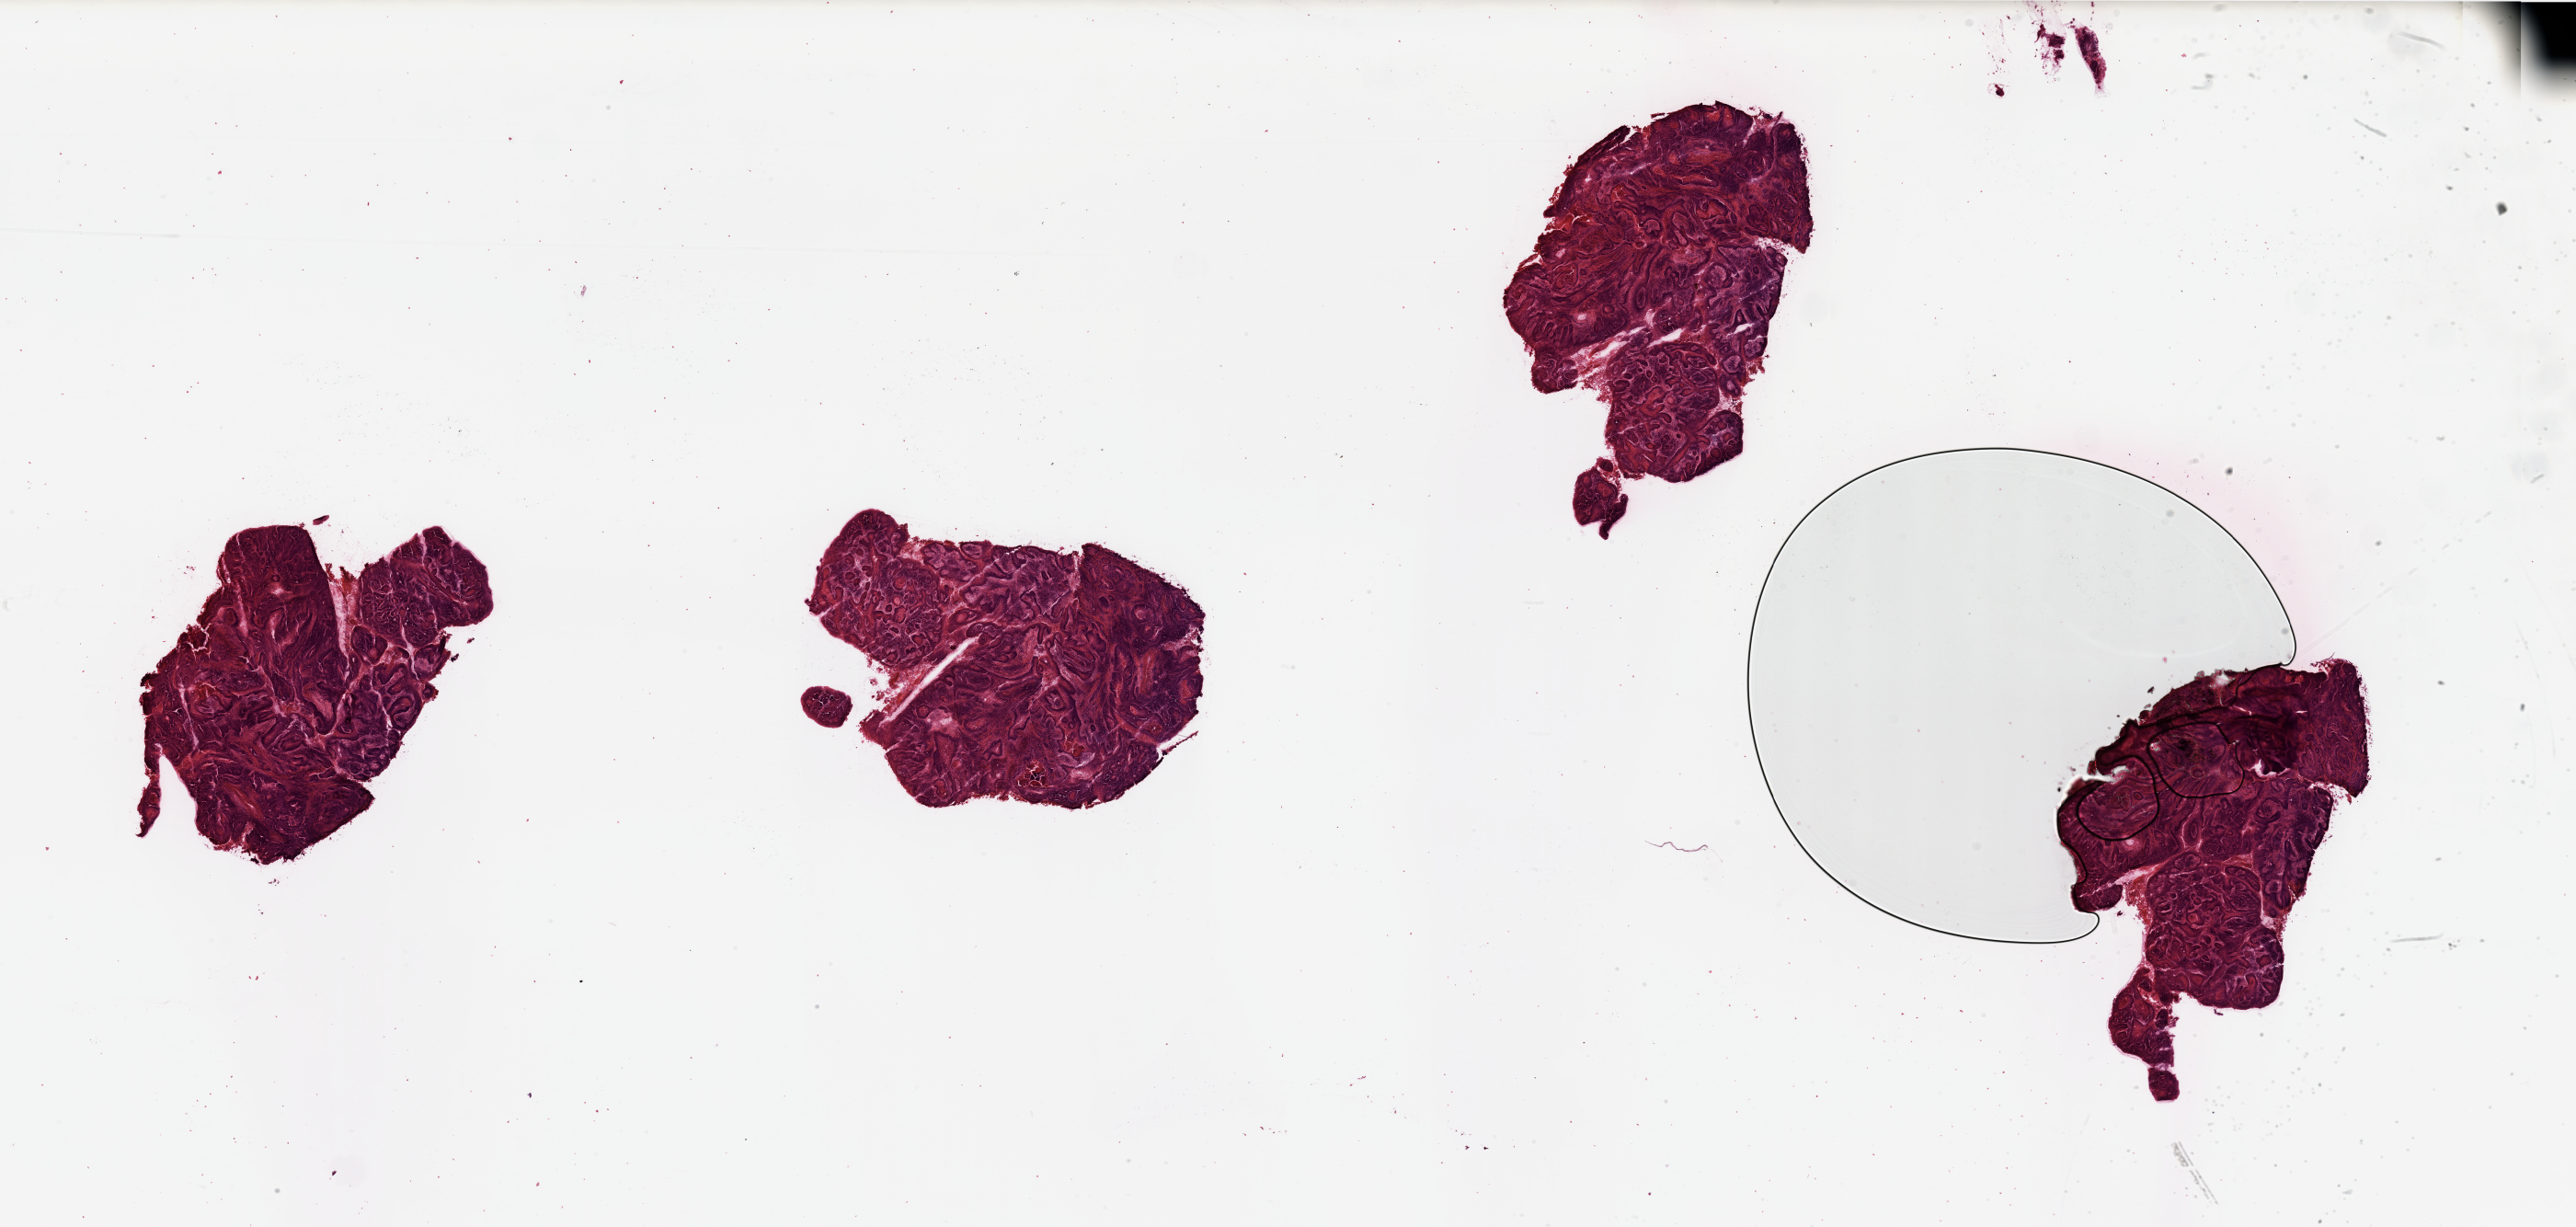
H&E whole-slide image, a low-resolution overview of the entire scanned area, about 44.3 x 21.1 mm (from a 20x scan), head and neck, tissue type not recorded. Male, 67 y/o.
• patient diagnosis: Squamous cell carcinoma, NOS